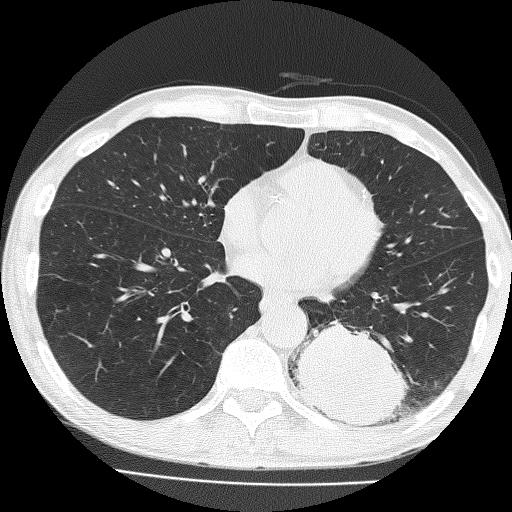
Low-dose screening chest CT, one axial slice; slice 67 of 160 in the series (ordered by position); reconstruction kernel FC51; lung window (W 1500 / L -600 HU); 2 mm slice thickness; 512 × 512 image matrix.
Outlined on this slice (expert manual segmentation):
- lesion 1 (tumor, lower lobe of left lung): bounding box <295,321,407,426> (left, top, right, bottom; pixels)